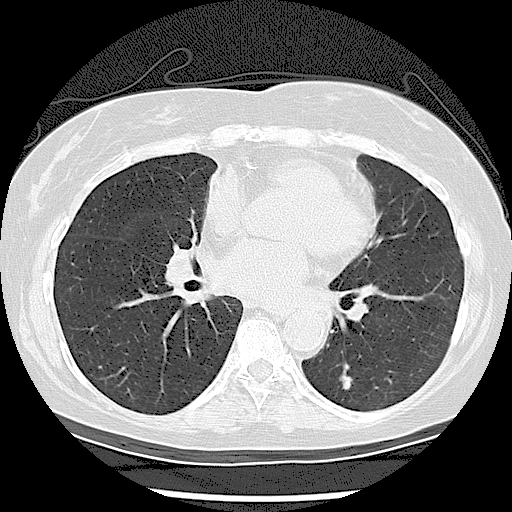
Chest CT (low-dose screening protocol), one axial image. Baseline annual screen. Lung window (W 1500 / L -600 HU). 2.5 mm slice thickness. Lung (sharp) reconstruction kernel (LUNG). Slice 63 of 108 in the series. Female participant, aged 61 years at enrolment. Current smoker at enrolment.
Expert-annotated lung lesion, bounding box <323,361,371,406> (left, top, right, bottom; pixels). The screening reader recorded 2 non-calcified nodules or masses ≥4 mm on this exam (left lower lobe, right lower lobe); which of them this box marks is not recorded.